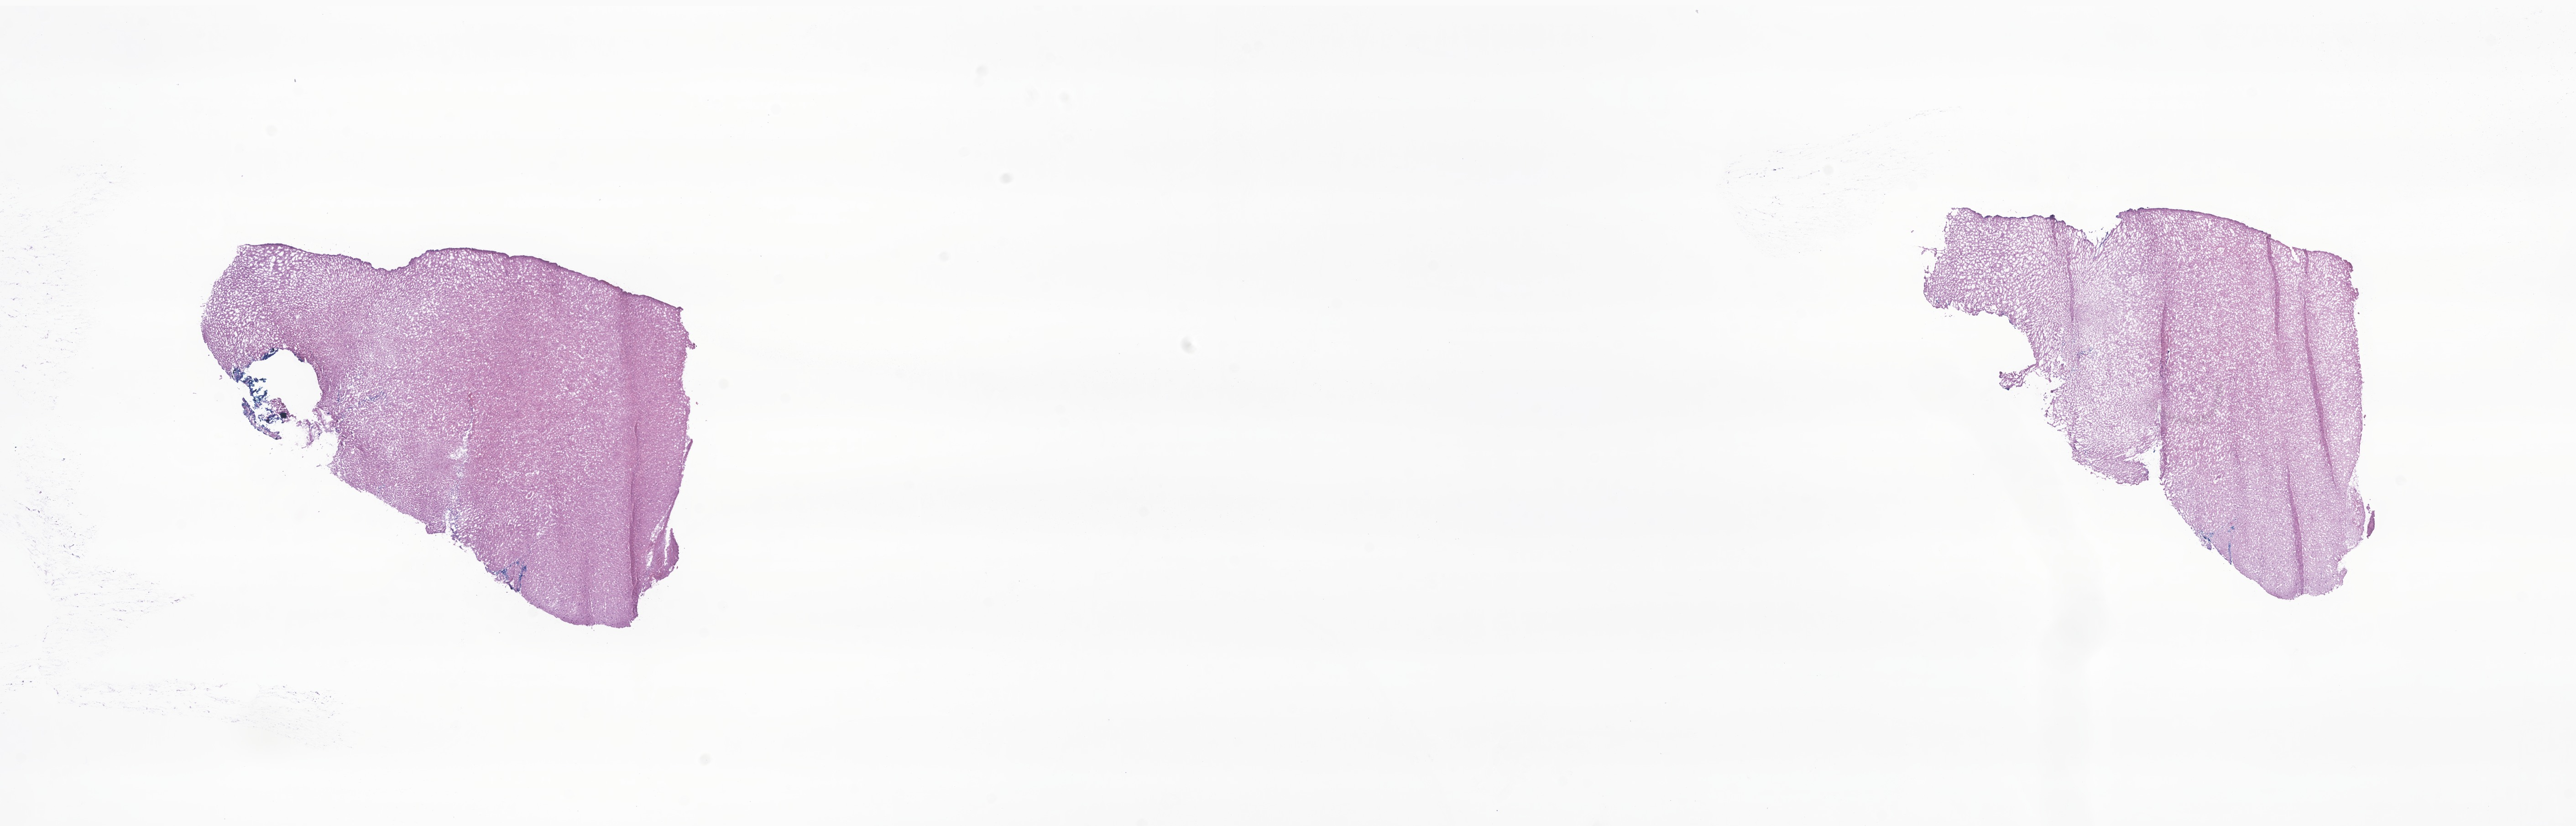
Whole-slide image, H&E stain of tumor tissue from the temporal lobe — a low-resolution overview of the entire scanned area, about 23.8 x 7.6 mm, frozen section (OCT-embedded). Male patient, age 565 days (about 1.5 years).
Diagnosis: Ganglioglioma, NOS.